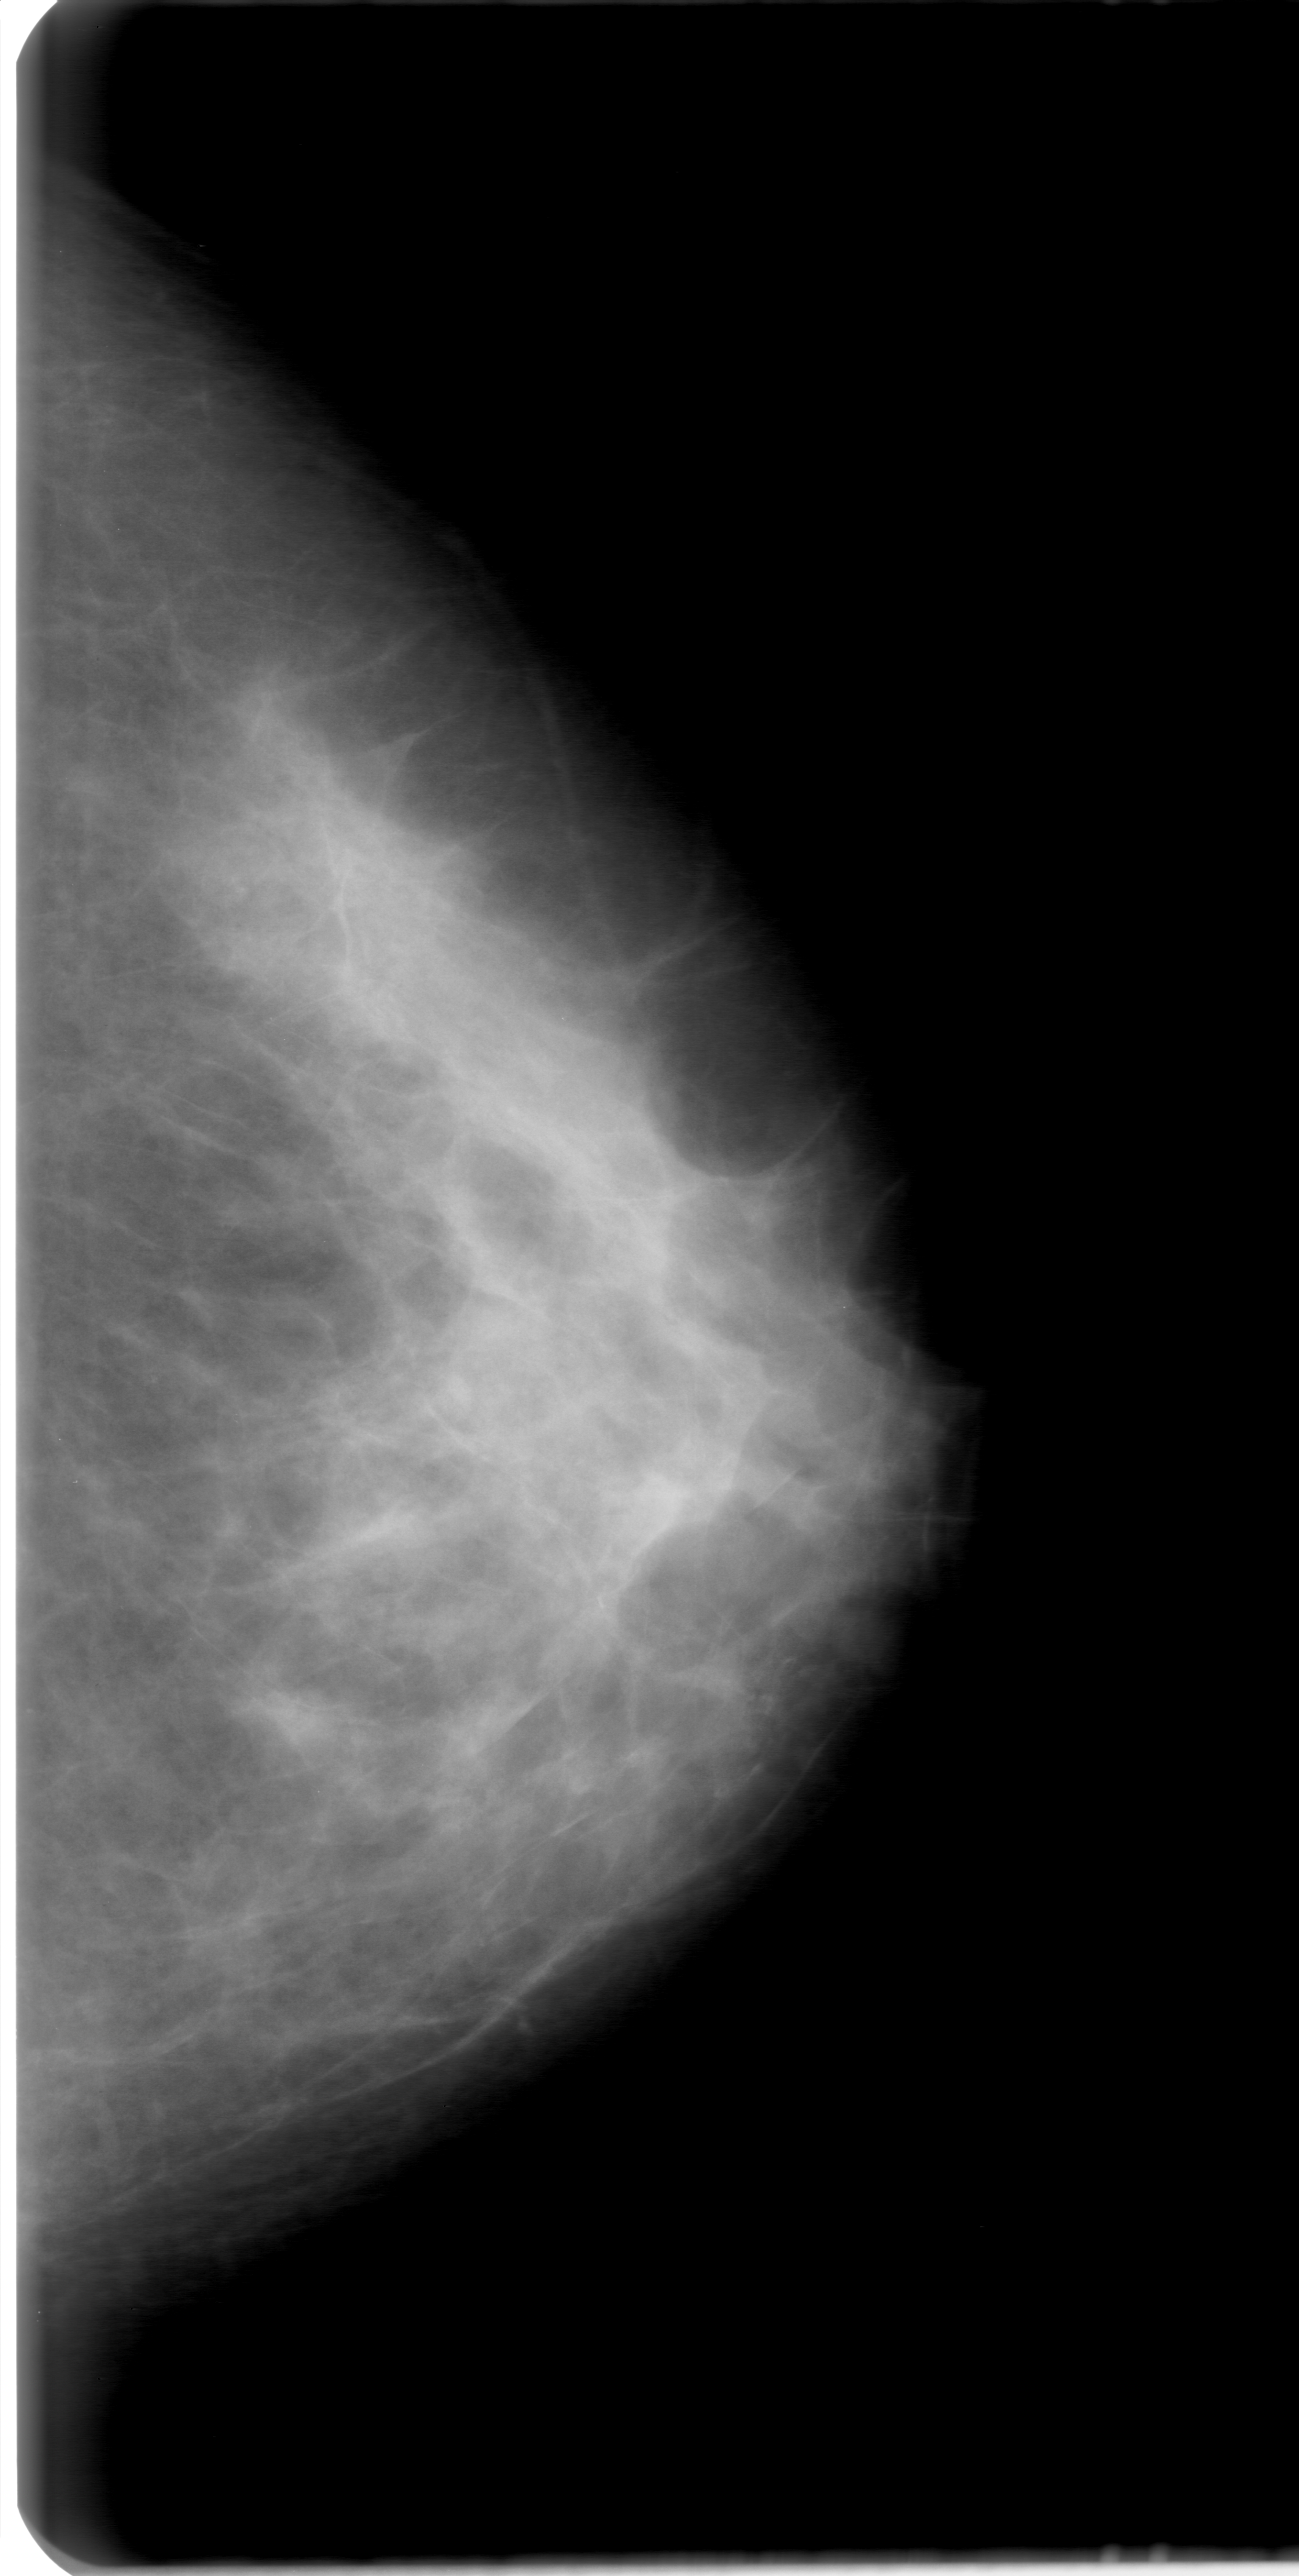
Mammogram (digitized film). Left breast. CC view. Breast composition: heterogeneously dense (BI-RADS density category 3 of 4). 1299 × 2576 image matrix.
Marked abnormalities (boxes around the expert regions of interest):
- calcifications, morphology amorphous, distribution segmental; BI-RADS assessment category 0 (incomplete: needs additional imaging); subtlety rating 1 on a 1 (subtle) to 5 (obvious) scale; pathology result (as recorded, not read from the image): benign: bounding box (x1, y1, x2, y2) in pixels: (81, 727, 723, 1333)